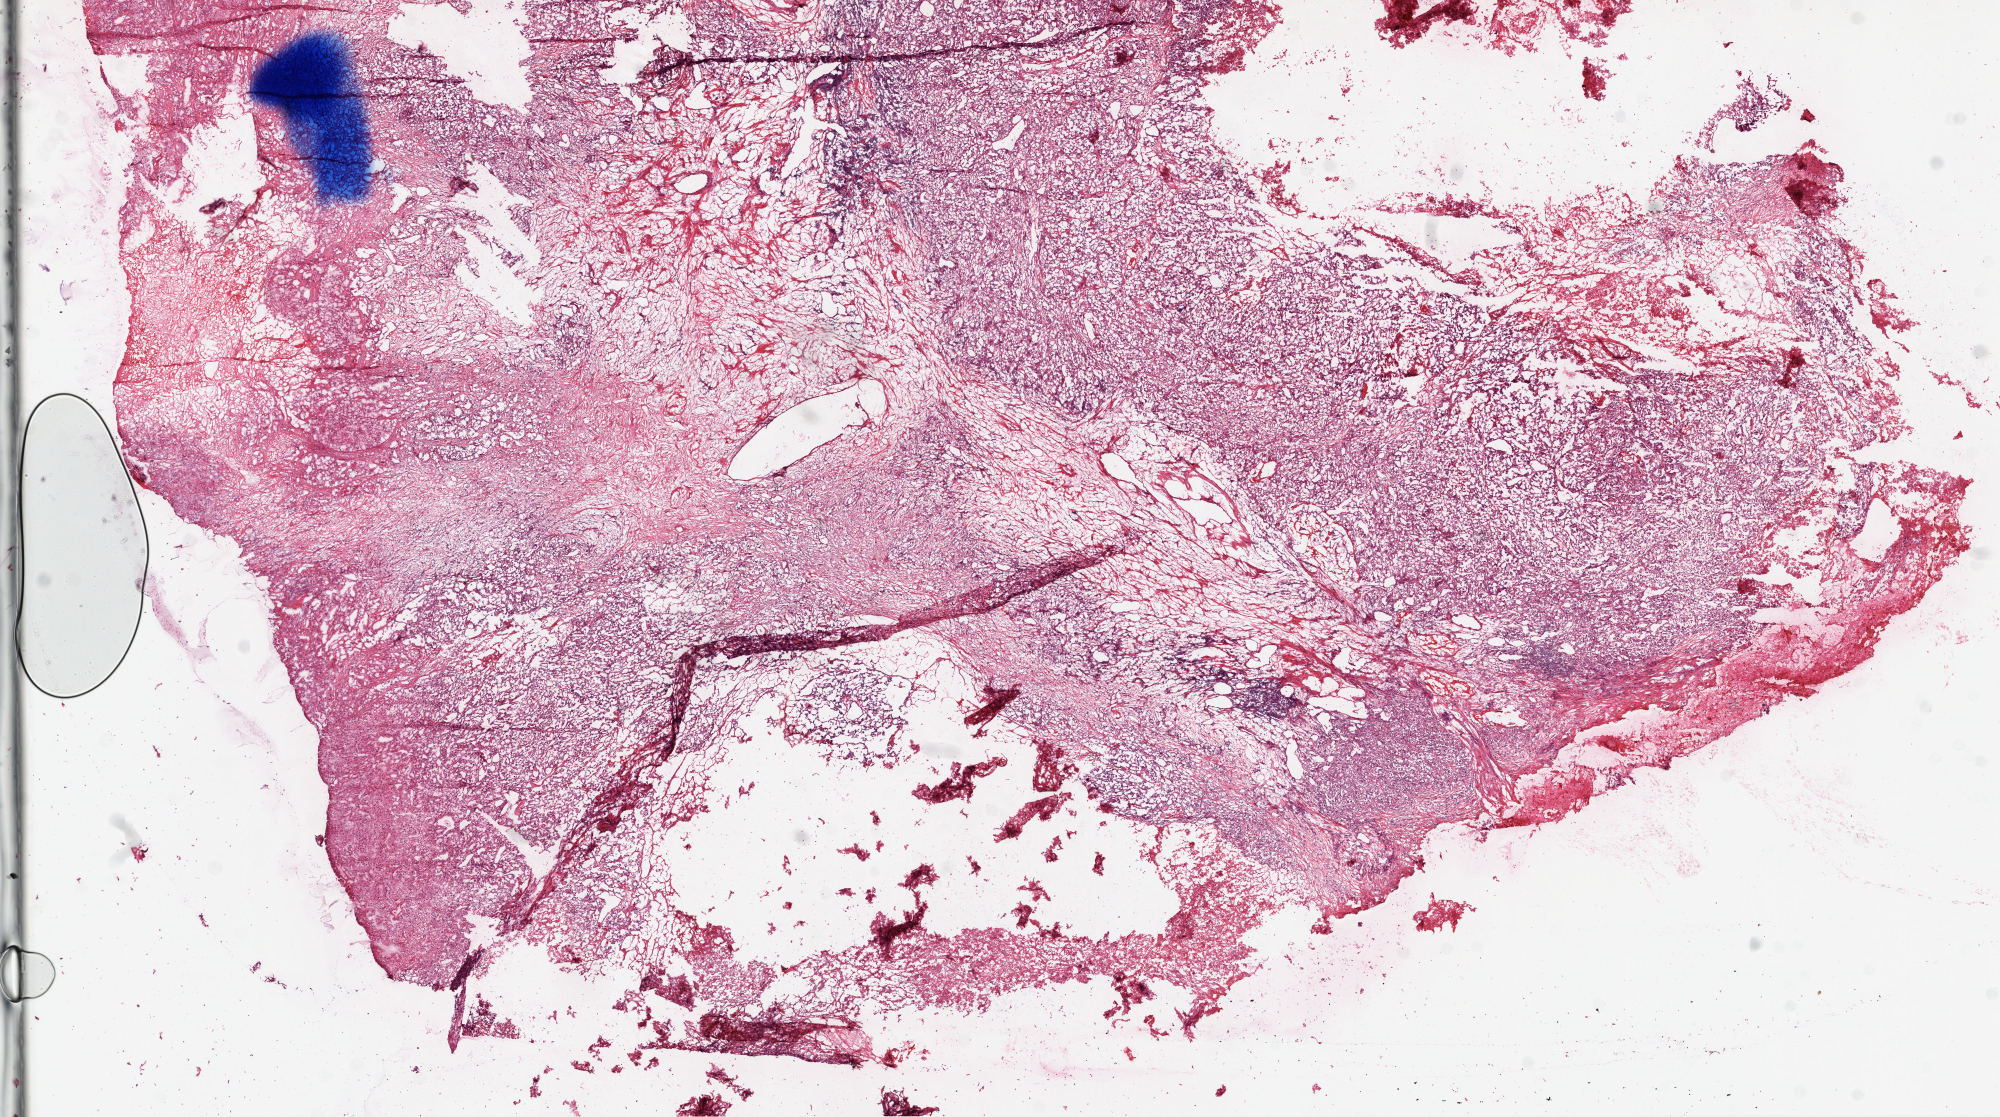
H&E whole-slide image, low-resolution overview of the scanned area, about 16.0 x 9.0 mm. Frozen section from the top of the tissue portion. Primary tumour sample from the kidney. Male patient; age at initial diagnosis 76 years. Histologic grade: G3 (poorly differentiated). Pathologist review of this section (percent, as recorded): tumour cells 65%, tumour nuclei 75%, normal cells 0%, stromal cells 30%, necrosis 5%.
AJCC pathologic stage: IV. Diagnosis: Clear cell adenocarcinoma, NOS.